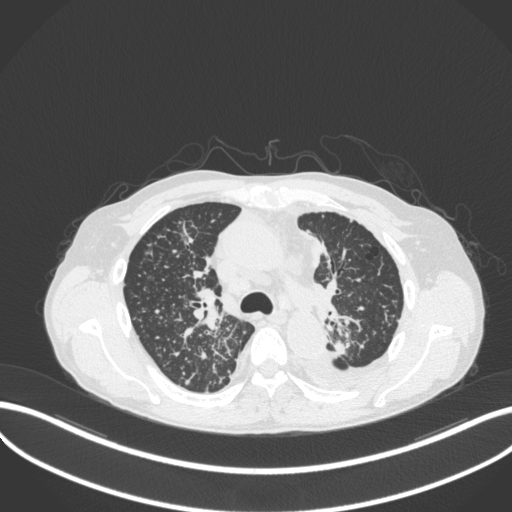
Chest CT, one axial slice. Slice 246 of 319 in the series (ordered by position). 120 kVp. Lung window (W 1500 / L -600 HU). 512 × 512 image matrix, field of view 400 × 400 mm. Male patient, age 58 years. From the clinical record (not read from this slice): clinical TNM (as recorded): T1c N3 M1.
Structures marked on this image (rectangle marked by the reading radiologist):
- lung tumour (recorded histology: adenocarcinoma): bounding box (x1, y1, x2, y2) in pixels: (326, 338, 353, 363)